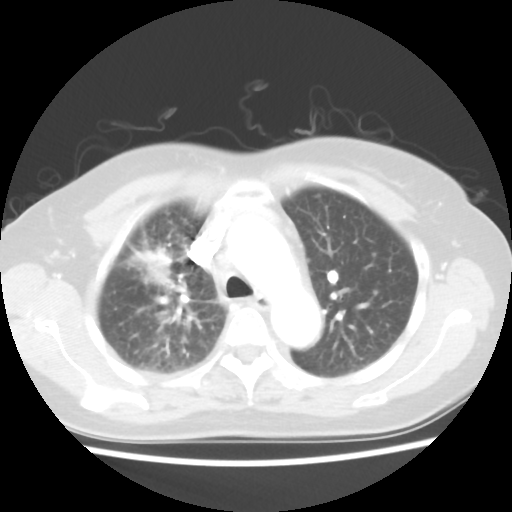
Chest CT, one axial slice. Slice 33 of 48 in the series (ordered by position). Reconstruction kernel STANDARD. Lung window (W 1500 / L -600 HU). 5 mm slice thickness. 512 × 512 image matrix, field of view 312 × 312 mm. Female patient, age 55 years. Case-level facts recorded for this patient, not image findings: clinical TNM (as recorded): T1b N3 M1a.
Annotated regions visible in this slice (rectangle marked by the reading radiologist):
- lung tumour (recorded histology: adenocarcinoma): bounding box (x1, y1, x2, y2) in pixels: (133, 245, 173, 284)